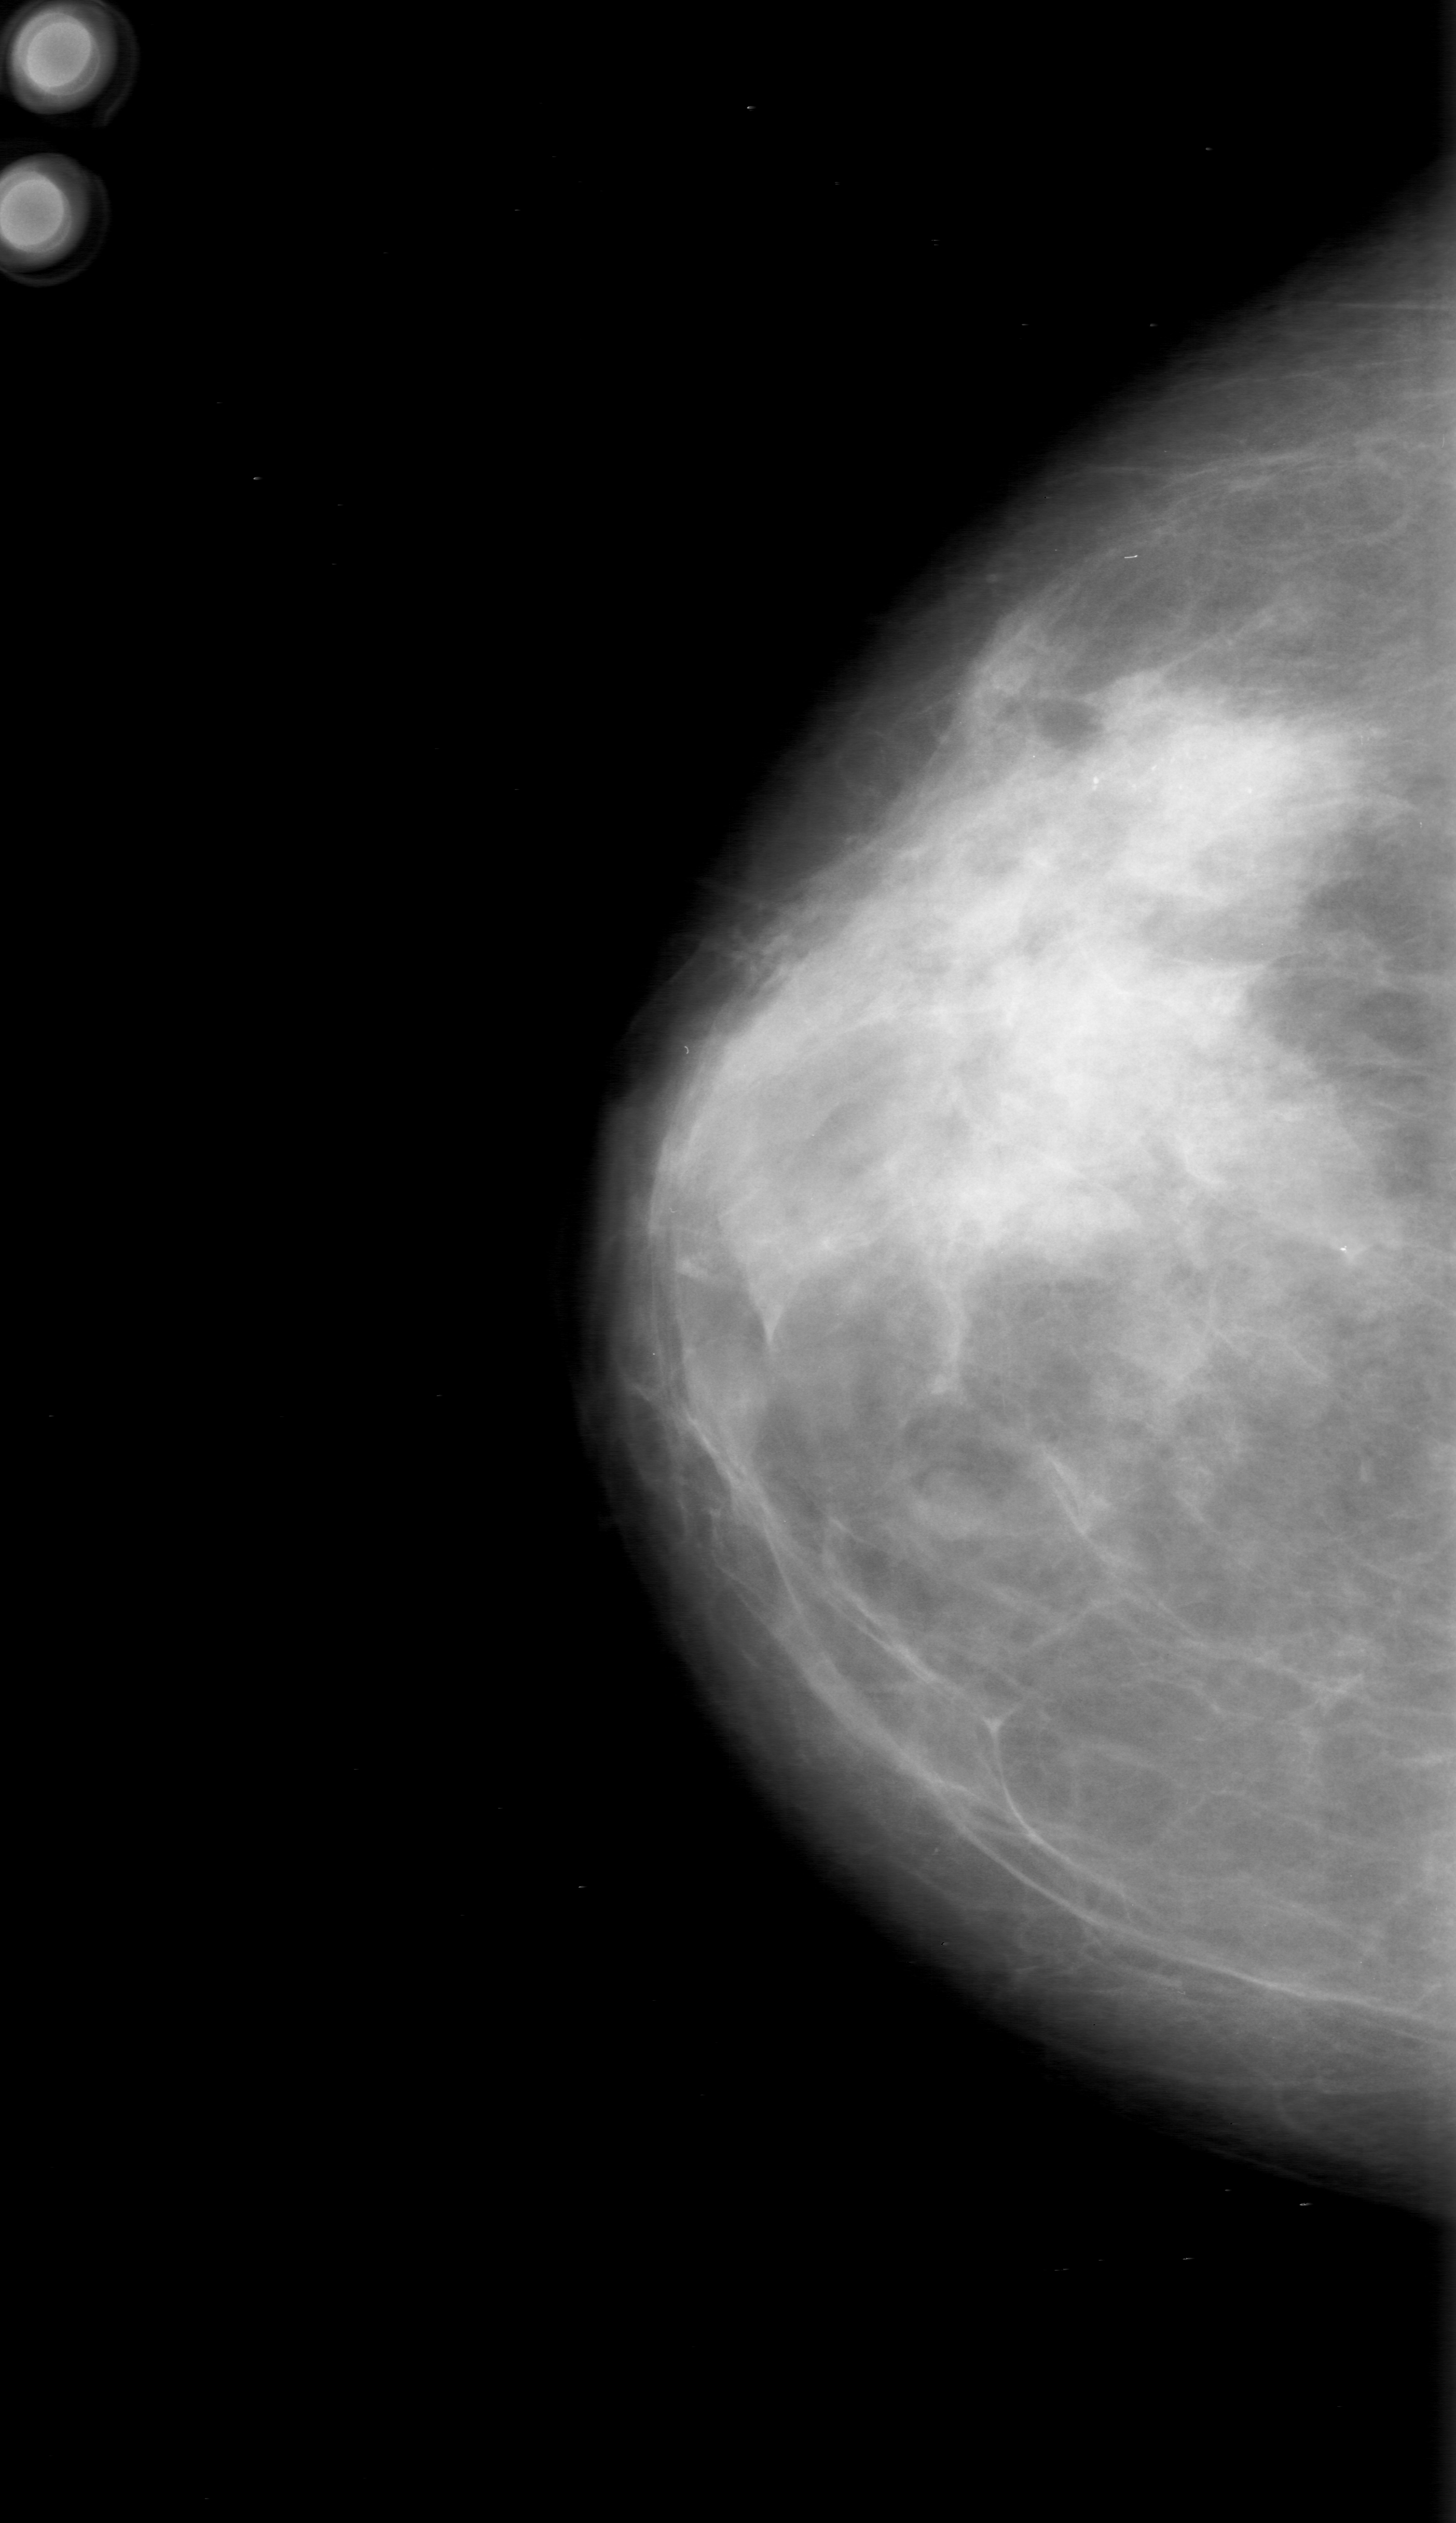
Digitized screen-film mammogram. Right breast. Craniocaudal (CC) view. BI-RADS breast density category 3 (scale 1–4). 1456 × 2523 image matrix.
Expert-marked regions of interest on this image (one box per marked abnormality):
- calcifications, morphology pleomorphic, distribution clustered; BI-RADS assessment category 0 (incomplete: needs additional imaging); pathology (as recorded): malignant: bounding box (x1, y1, x2, y2) in pixels: (920, 656, 1368, 946)